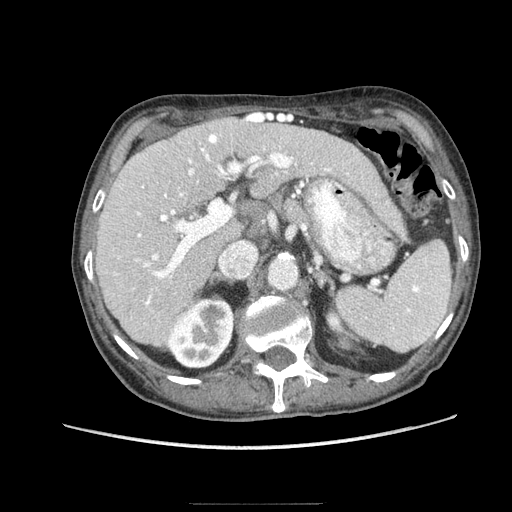
Contrast-enhanced abdominal CT (liver protocol), one axial slice; slice 50 of 83 in the series (ordered by position); soft-tissue window (W 400 / L 40 HU); 2.5 mm slice thickness; 512 × 512 image matrix, field of view 360 × 360 mm. From the clinical record (not read from this slice): diagnosis: hepatocellular carcinoma (patient treated with transarterial chemoembolisation; whether this scan precedes or follows treatment is not stated here); TNM stage (as recorded): Stage-I; Child-Pugh class: A; tumour differentiation: moderately differentiated; tumour nodularity: uninodular.
Outlined on this slice (semi-automatic segmentation, software-assisted and operator-edited):
- liver parenchyma outside the tumour (the mass and vessels are separate outlines, so this box may not span the whole liver): bounding box (x1, y1, x2, y2) in pixels: (96, 114, 367, 346)
- liver vessels: (114, 114, 348, 306)